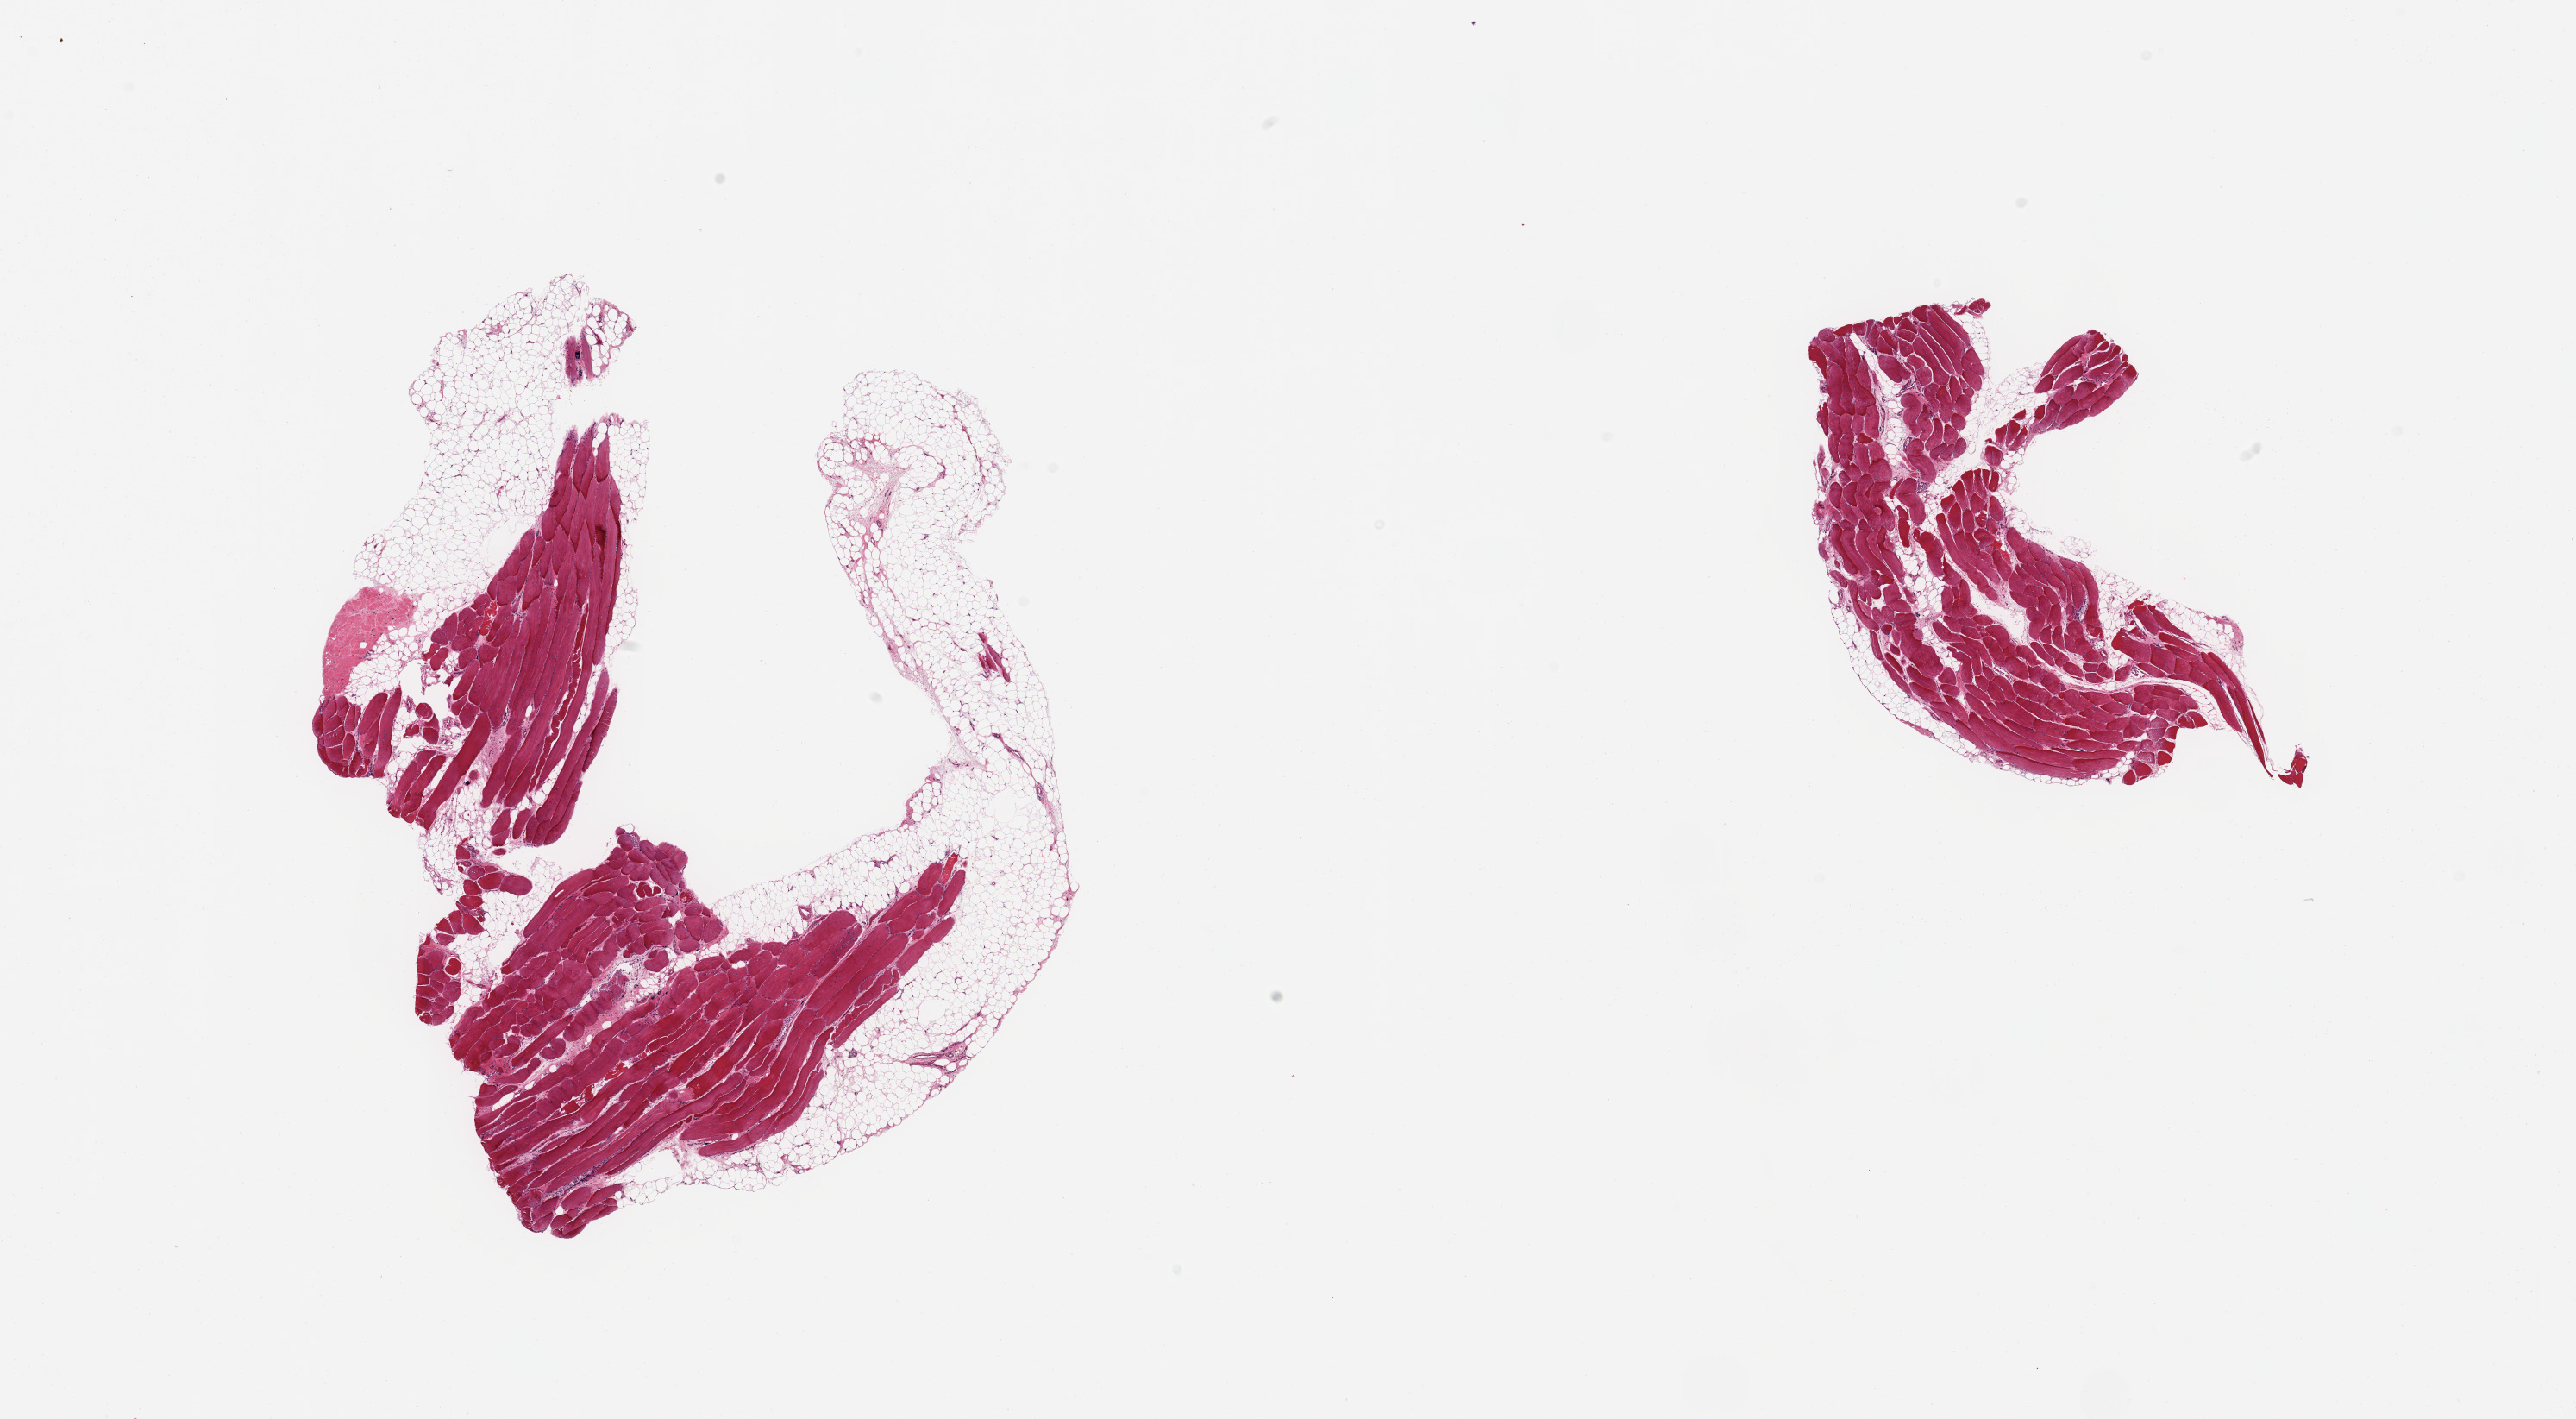
Haematoxylin and eosin whole-slide image — shown as a low-resolution overview of the whole scanned area (about 23.6 x 13.0 mm, slide scanned at 20x). PAXgene-fixed paraffin-embedded (PFPE) section. Target tissue: skeletal muscle. Tissue donor sample. Male donor.
Review note (as recorded): 2 pieces; 40 & 10% internal & external fat.